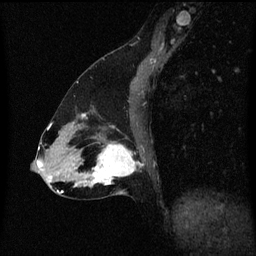
Breast MRI (dynamic contrast-enhanced), one sagittal slice; position 28 of 60 along the scan axis; dynamic contrast-enhanced series, image 2 of 3 at this slice position (ordered by acquisition); 1.5 T; TE 4.2 ms, TR 8.4 ms; 256 × 256 image matrix. Female patient, age 47 years.
Outlined on this slice (semi-automatically segmented with operator editing):
- analysis volume of interest (the breast-tissue region the enhancement analysis was run in; not a lesion): bounding box (x1, y1, x2, y2) in pixels: (85, 136, 136, 195)
- tumour enhancement mask (voxels above the 70 % enhancement threshold inside the analysis volume of interest): (85, 144, 136, 187)